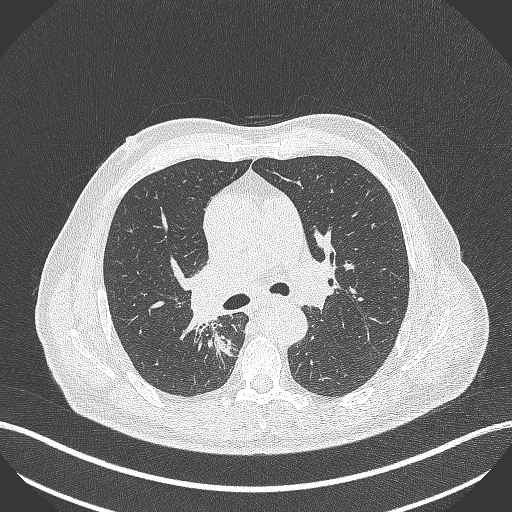
Chest CT, one axial slice; slice 286 of 451 in the series (ordered by position); 100 kVp; lung window (W 1500 / L -600 HU); 1 mm slice thickness; 512 × 512 image matrix, field of view 400 × 400 mm. Patient: male, 61 years. Case-level facts recorded for this patient, not image findings: clinical TNM (as recorded): T1 N0 M0.
Structures marked on this image (rectangle marked by the reading radiologist):
- lung tumour (recorded histology: small cell carcinoma): bounding box [x1, y1, x2, y2] px = [210, 328, 236, 356]